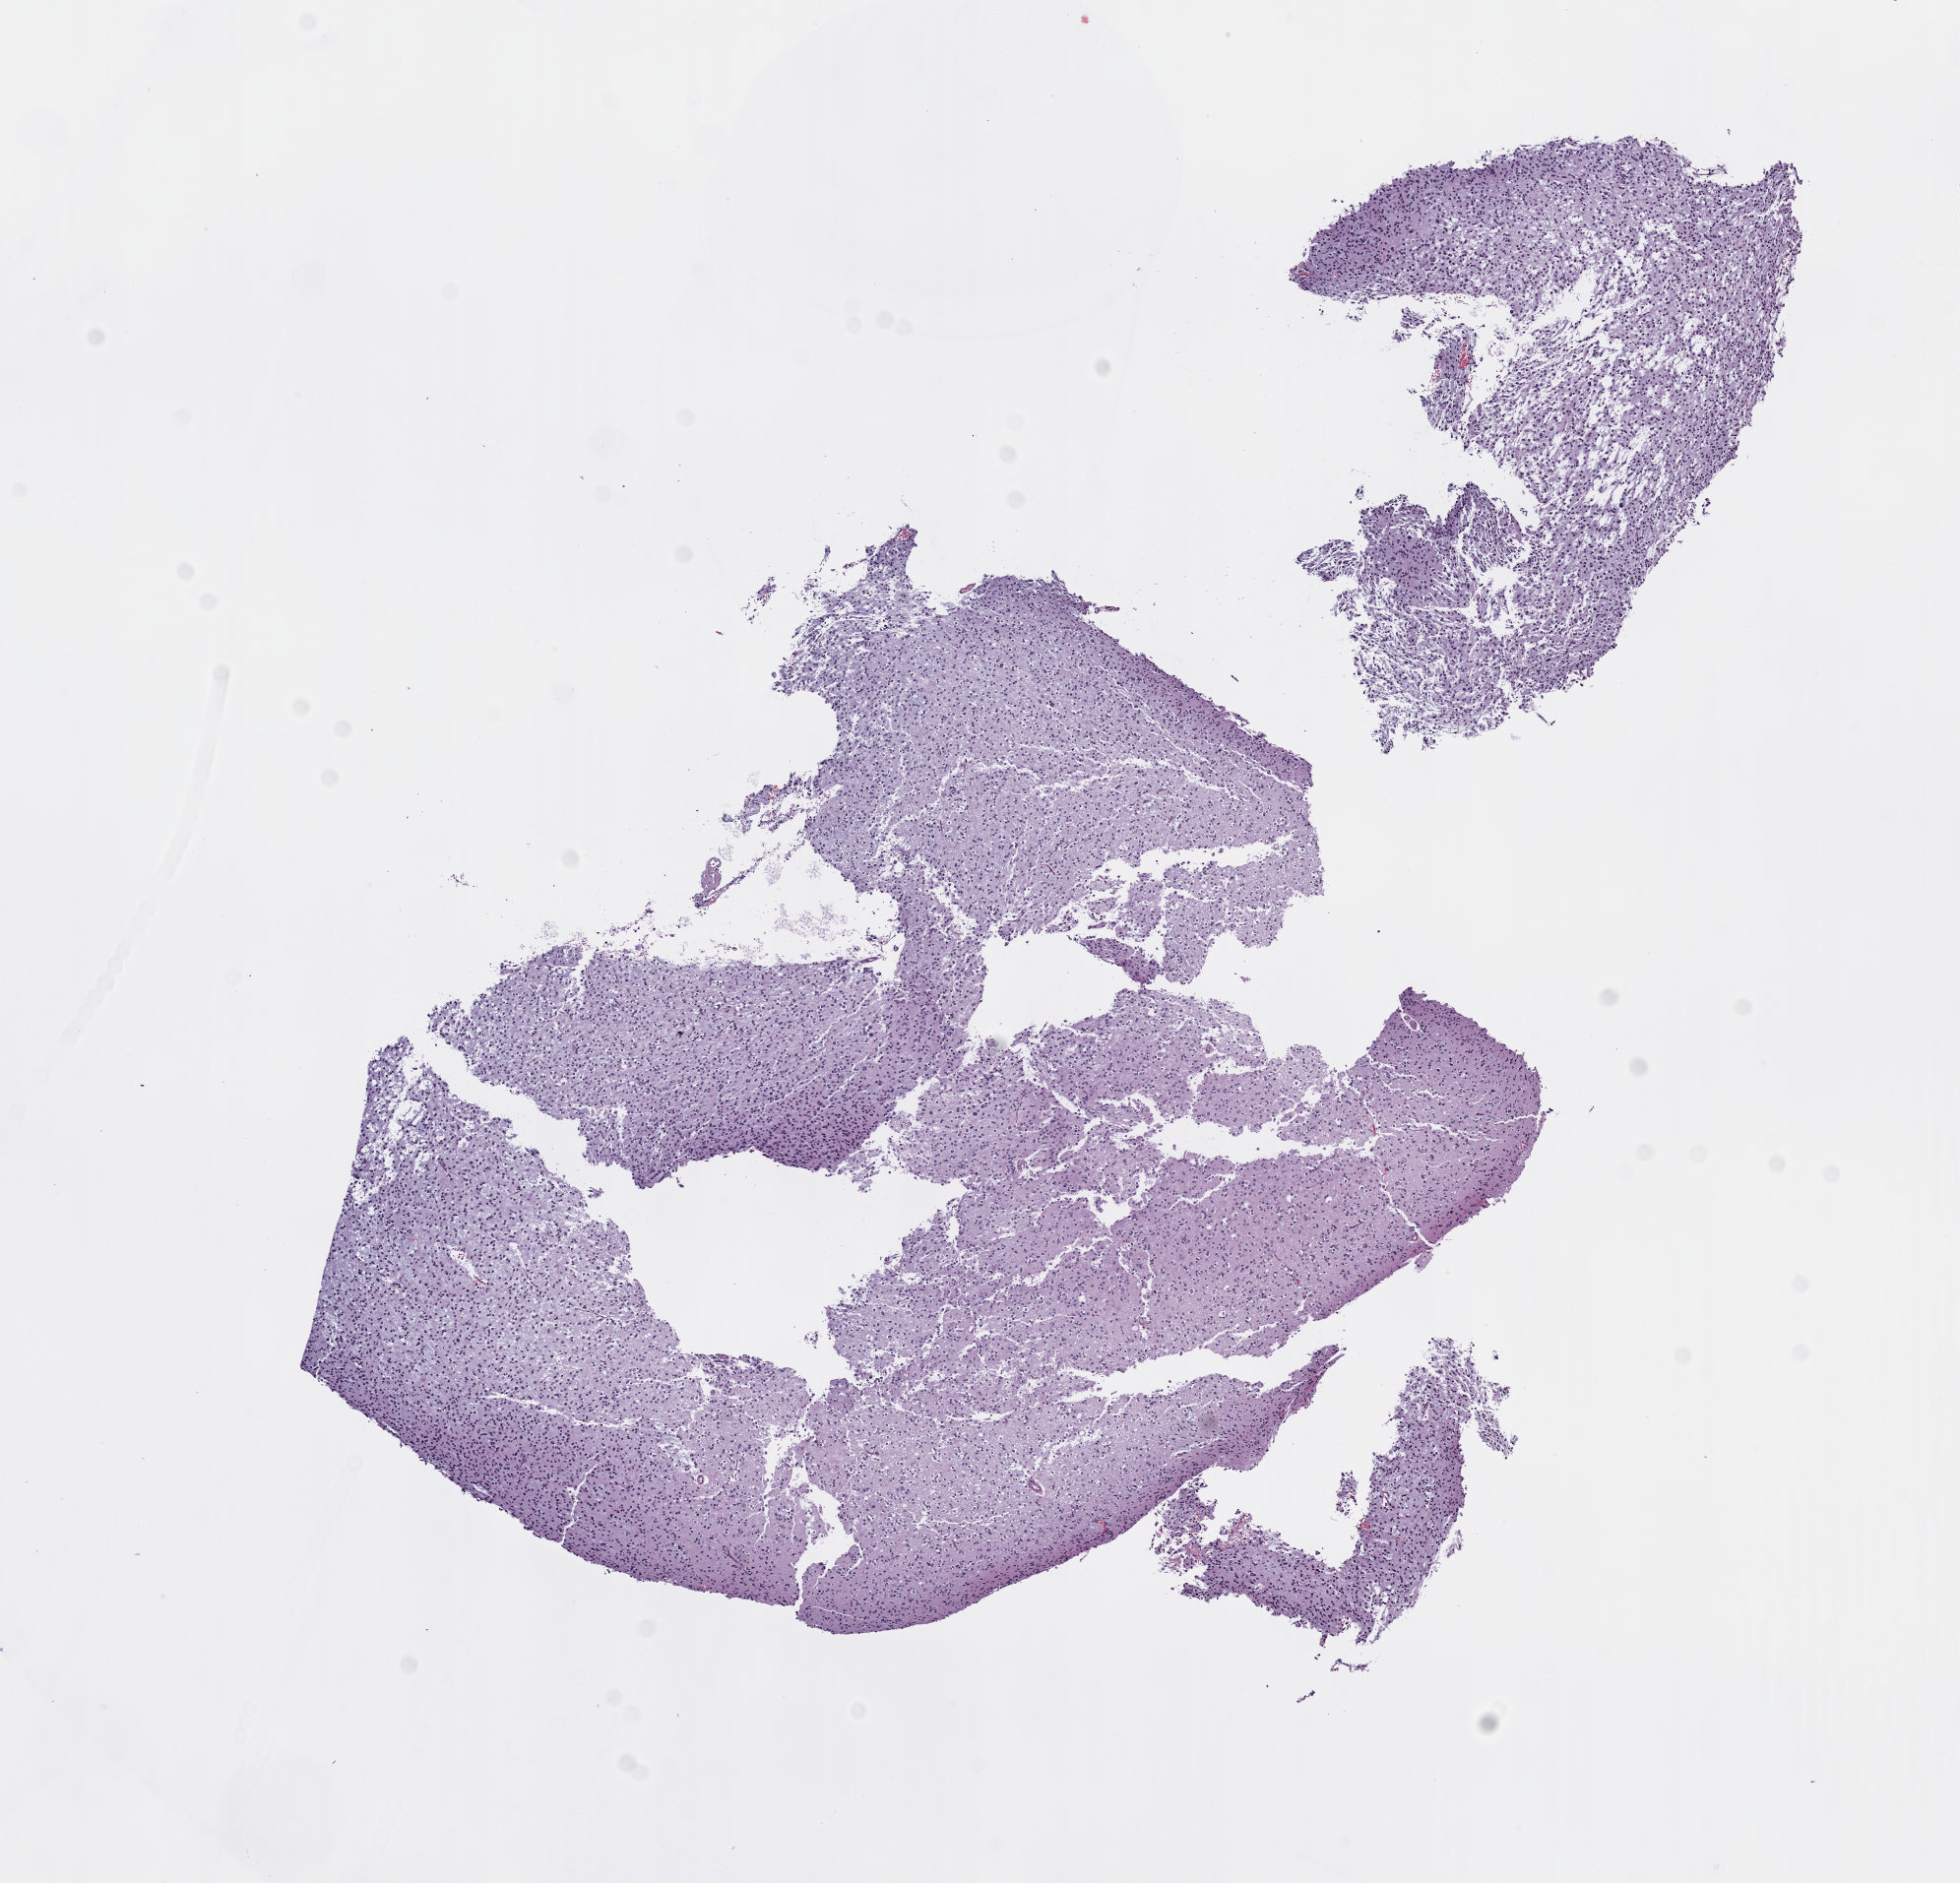
Digitized H&E tissue section (whole slide) — whole scanned area (about 8.1 x 7.7 mm) shown as a low-resolution overview; FFPE section; primary tumour sample from the brain. Patient: female, age at initial diagnosis 50 years.
Histologic diagnosis: Oligodendroglioma, NOS (cerebrum).